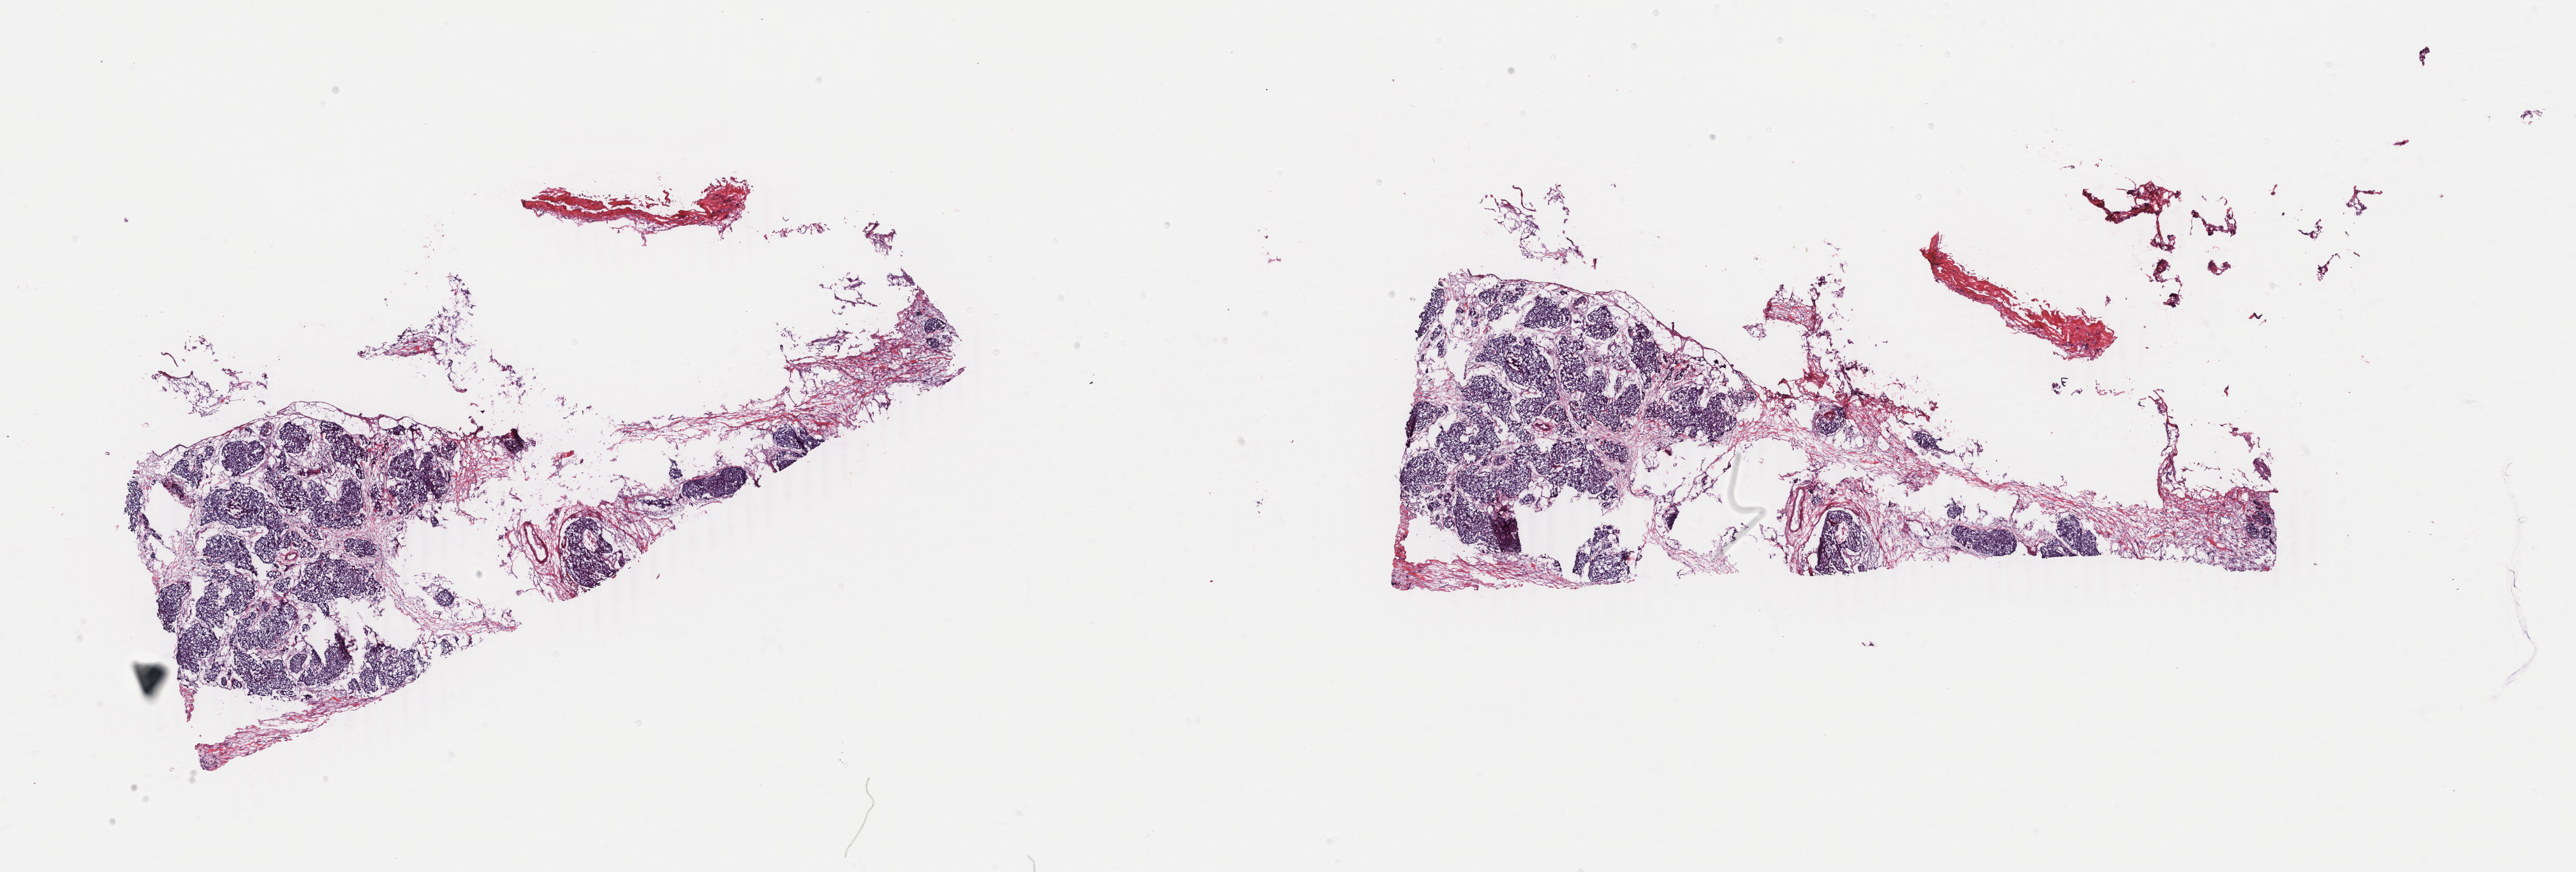
Hematoxylin and eosin (H&E) stained whole-slide image — shown as a low-resolution overview of the whole scanned area (about 32.1 x 10.9 mm, from a 40x scan); frozen section; sample: primary tumour, bladder. Patient: male, age at initial diagnosis 75 years. Histologic grade: high grade. Pathologist review of this section (percent, as recorded): tumour cells 80%, tumour nuclei 80%, normal cells 0%, stromal cells 20%, necrosis 0%. Infiltration values recorded for this section: lymphocyte infiltration 3%, monocyte infiltration 0%, neutrophil infiltration 0%.
Histologic diagnosis: Transitional cell carcinoma. AJCC pathologic stage: III (6th edition). Lymph nodes positive (case pathology): 0 of 24 examined.